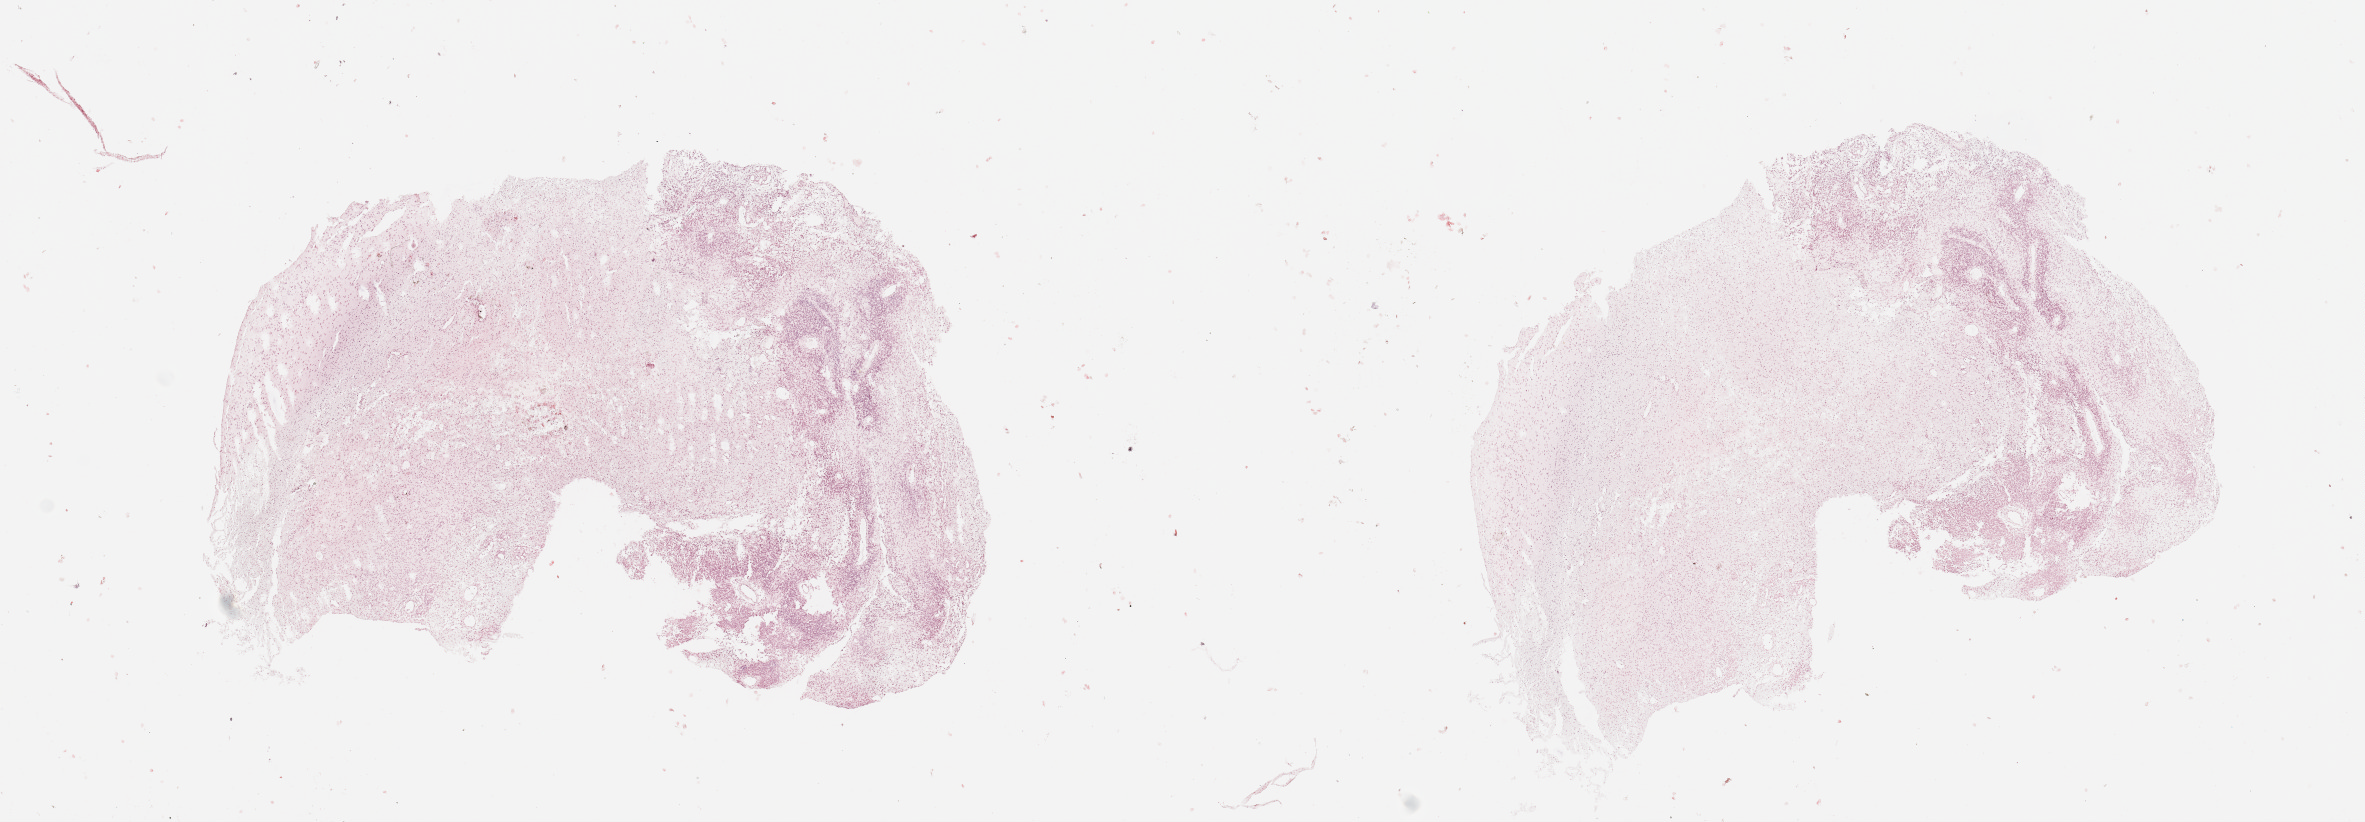
Digitized H&E-stained tissue section (whole slide) — low-resolution overview of the scanned area, about 18.7 x 6.5 mm (from a 20x scan). Tumour tissue sample, sampled site: occipital cortex. 88-year-old male patient.
Diagnosis: Glioblastoma.